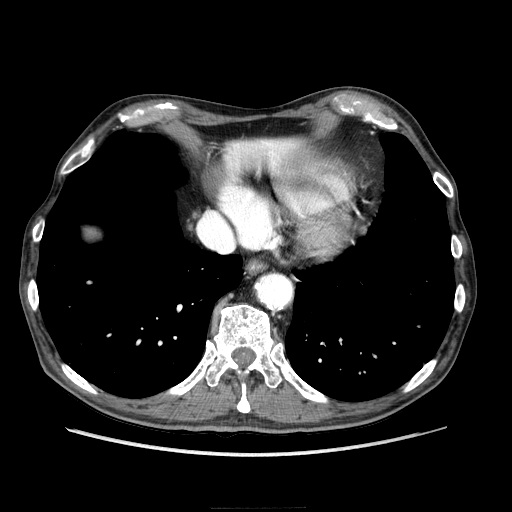
Contrast-enhanced abdominal CT (liver protocol), one axial slice. Slice 197 of 218 in the series (ordered by position). 100 kVp. Soft-tissue window (W 400 / L 40 HU). 2.5 mm slice thickness. 512 × 512 image matrix, field of view 380 × 380 mm. From the clinical record (not read from this slice): diagnosis: hepatocellular carcinoma (patient treated with transarterial chemoembolisation; whether this scan precedes or follows treatment is not stated here); TNM stage (as recorded): Stage-IIIA; Child-Pugh class: A; tumour differentiation: well differentiated; tumour nodularity: multinodular.
Outlined on this slice (semi-automatic segmentation, software-assisted and operator-edited):
- liver parenchyma outside the tumour (the mass and vessels are separate outlines, so this box may not span the whole liver): box from (x=87, y=229) to (x=95, y=236) px